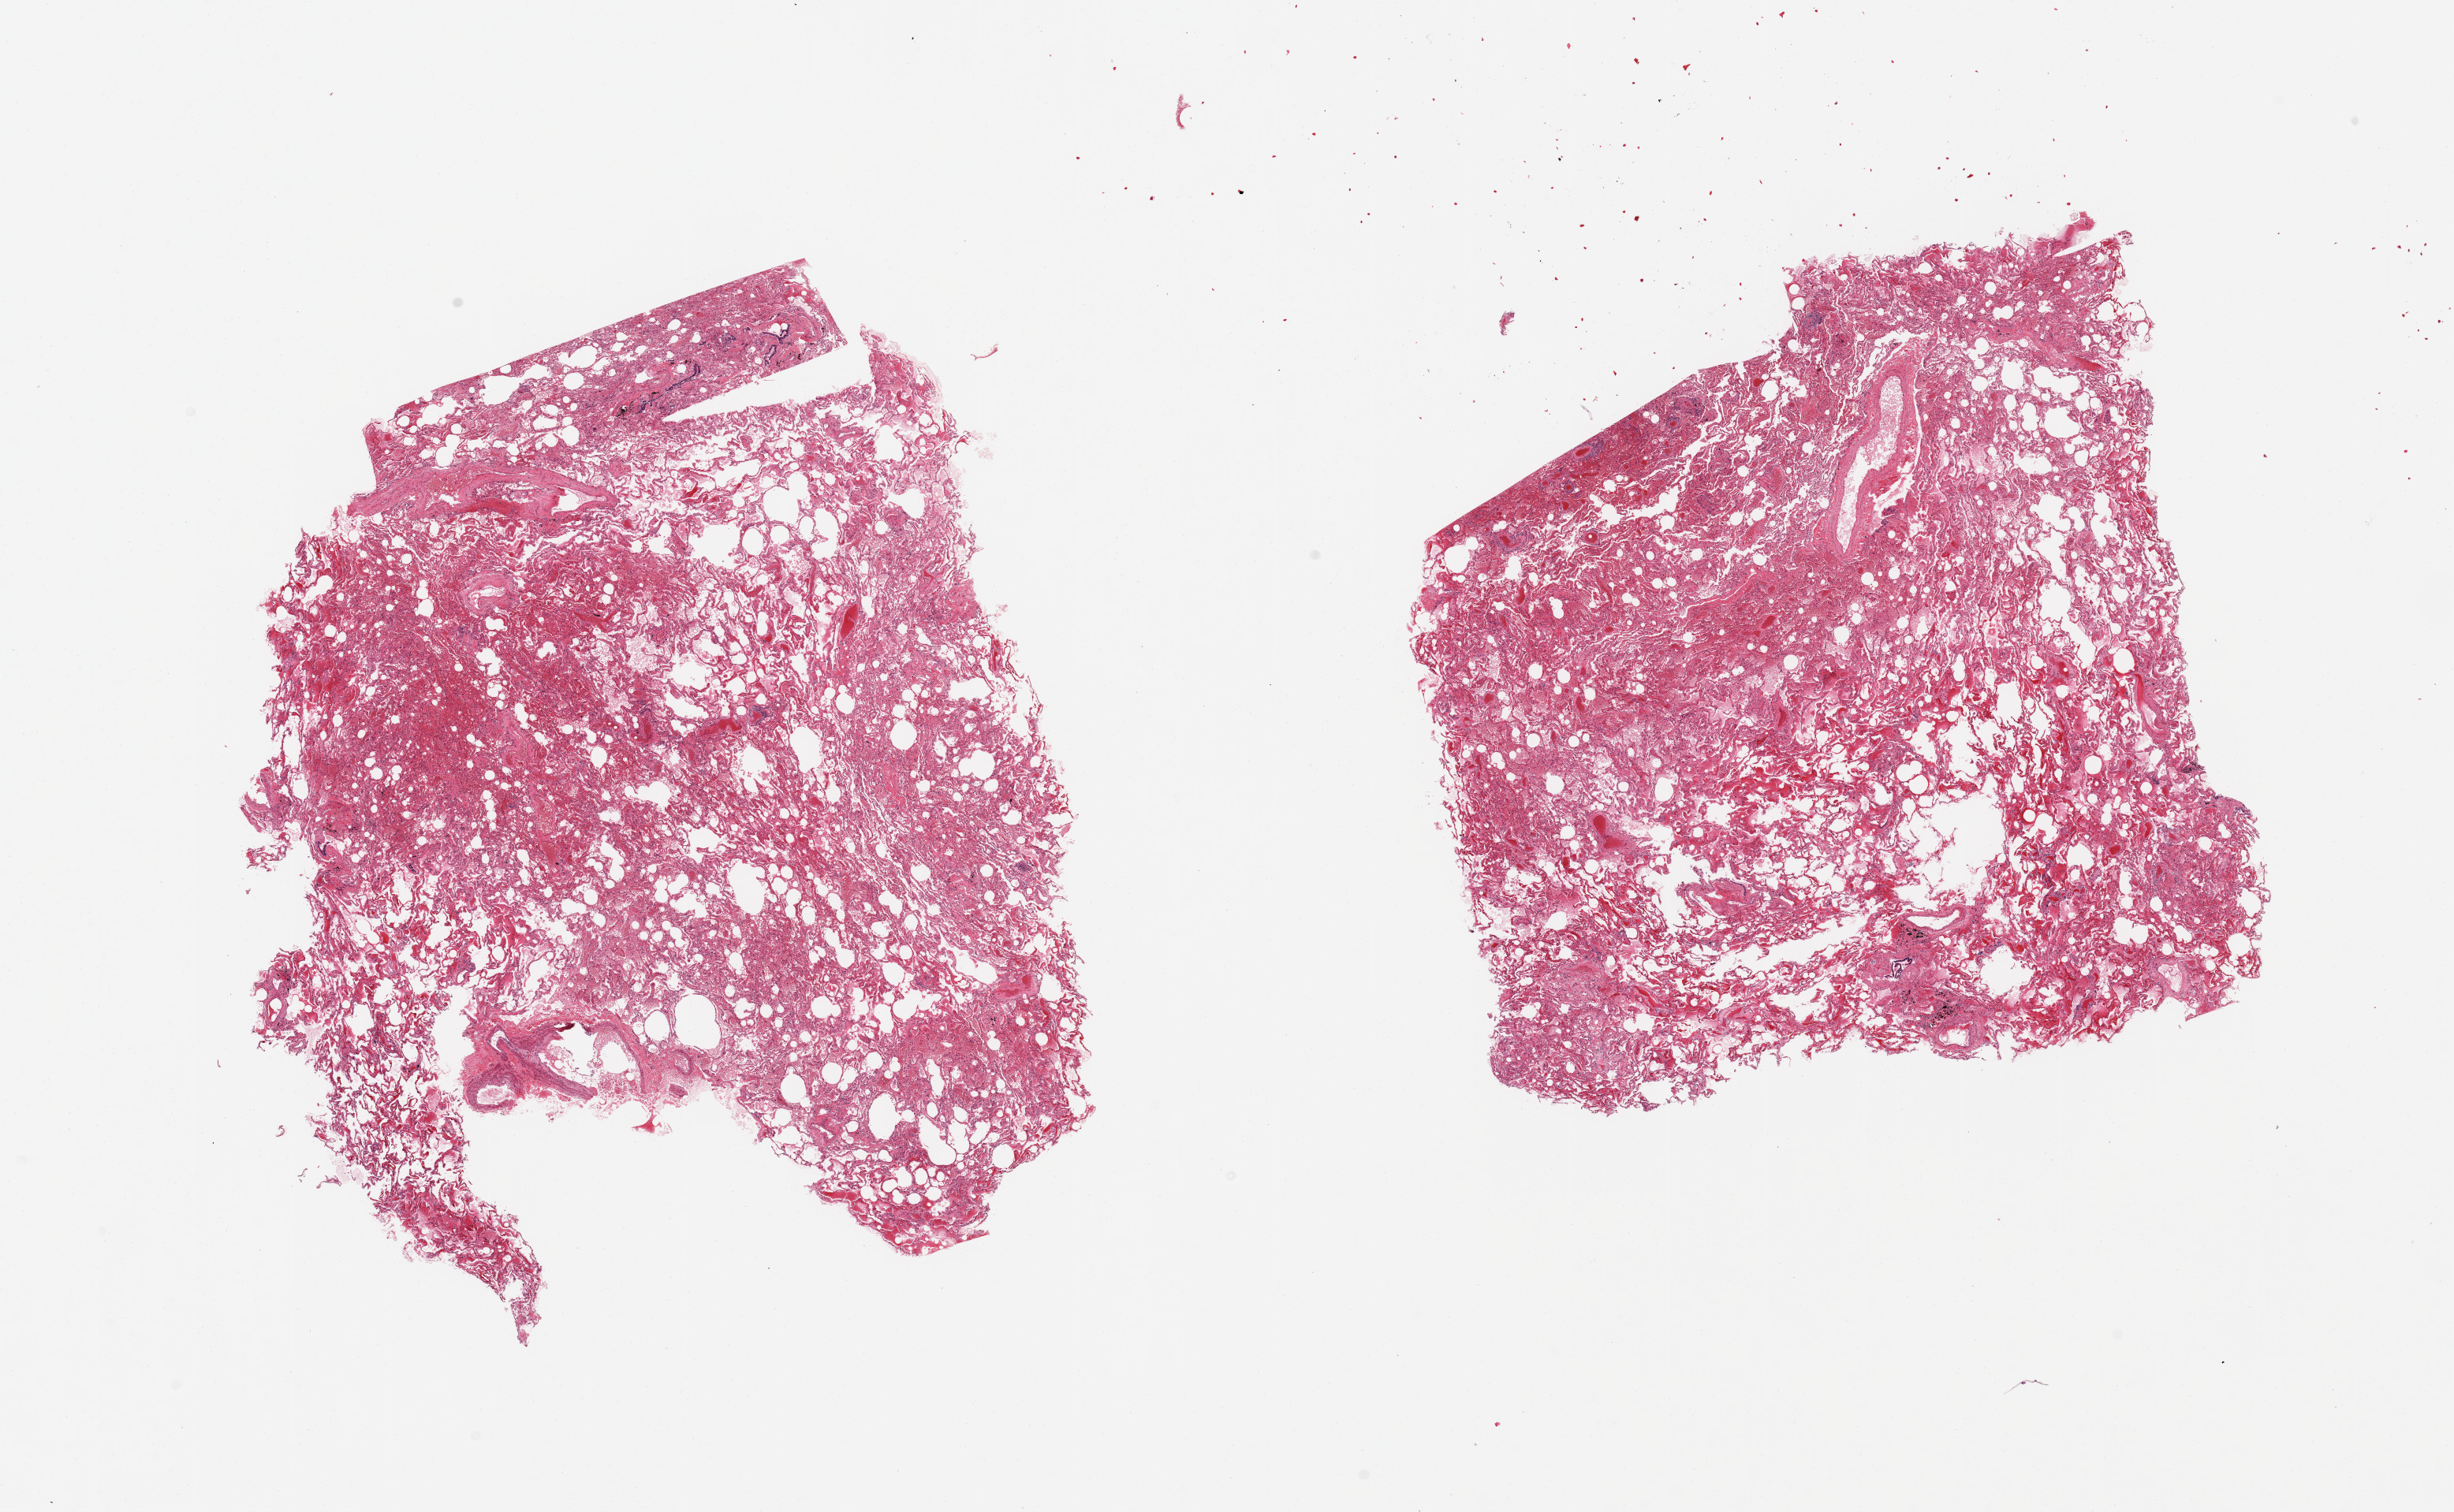
H&E whole-slide image — whole scanned area (about 24.6 x 15.2 mm, from a 20x scan) shown as a low-resolution overview; PAXgene-fixed, paraffin-embedded tissue; sampled site (target tissue): lung; donor tissue sample.
• review note (as recorded): 2 pieces; congestion and hemorrhage